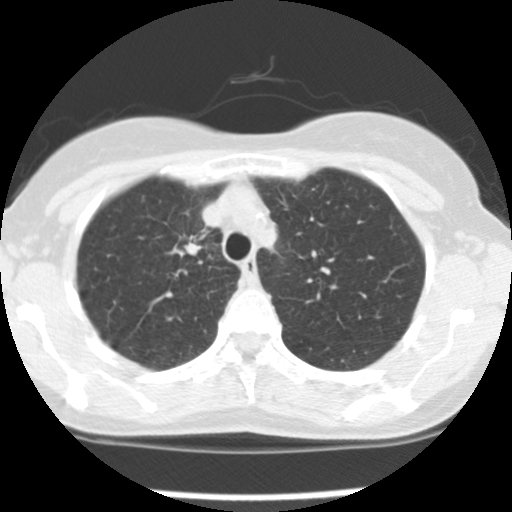
Low-dose screening chest CT, one axial slice. Slice 120 of 157 in the series (ordered by position). Reconstruction kernel STANDARD. 120 kVp. Lung window (W 1500 / L -600 HU). 2.5 mm slice thickness. 512 × 512 image matrix.
Annotated regions visible in this slice (manually delineated by an expert):
- lesion 1 (tumor, upper lobe of right lung): bounding box (x1, y1, x2, y2) in pixels: (173, 235, 202, 256)